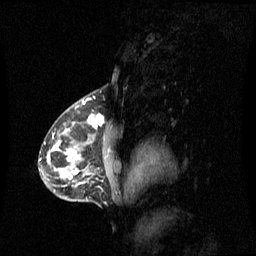
Breast MRI (dynamic contrast-enhanced), one sagittal slice. Slice 41 of 60 in the series (ordered by position). Dynamic contrast-enhanced series, image 2 of 3 at this slice position (ordered by acquisition). 1.5 T. TE 4.2 ms, TR 8.4 ms. 2 mm slice thickness. 256 × 256 image matrix. Patient: female, 42 years. From the clinical record (not read from this slice): setting: breast cancer imaged before/during neoadjuvant chemotherapy; receptor status: HR-positive, HER2-negative.
Annotated regions visible in this slice (semi-automatically segmented with operator editing):
- analysis volume of interest (the breast-tissue region the enhancement analysis was run in; not a lesion): bounding box <56,114,120,185> (left, top, right, bottom; pixels)
- tumour enhancement mask (voxels above the 70 % enhancement threshold inside the analysis volume of interest): <66,114,104,179>